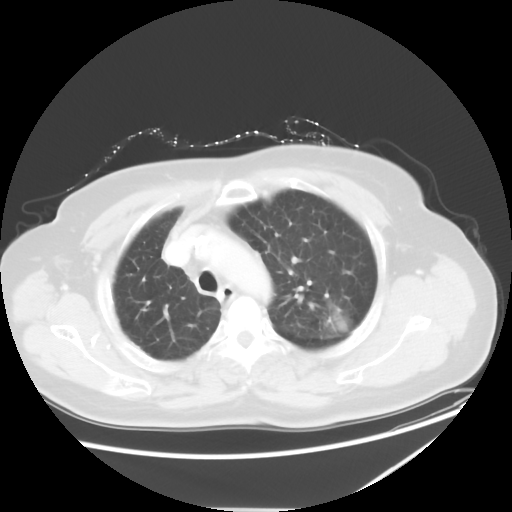
Chest CT, one axial slice; slice 41 of 54 in the series (ordered by position); 120 kVp; lung window (W 1500 / L -600 HU); 5 mm slice thickness; 512 × 512 image matrix, field of view 384 × 384 mm. Patient: female, 61 years. Case-level facts recorded for this patient, not image findings: clinical TNM (as recorded): T1c N3 M1.
Outlined on this slice (bounding box drawn by a radiologist):
- lung tumour (recorded histology: adenocarcinoma): bounding box (x1, y1, x2, y2) in pixels: (312, 298, 358, 341)